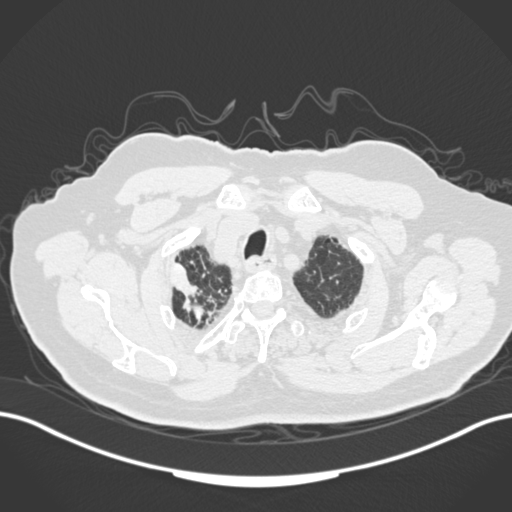
Chest CT, one axial slice; position 153 of 205 along the scan axis; 120 kVp; lung window (W 1500 / L -600 HU); 1 mm slice thickness; 512 × 512 image matrix. Patient: male, 72 years. Case-level facts recorded for this patient, not image findings: clinical TNM (as recorded): T1a N0 M0.
Outlined on this slice (rectangle marked by the reading radiologist):
- lung tumour (recorded histology: squamous cell carcinoma): bounding box <170,259,209,323> (left, top, right, bottom; pixels)